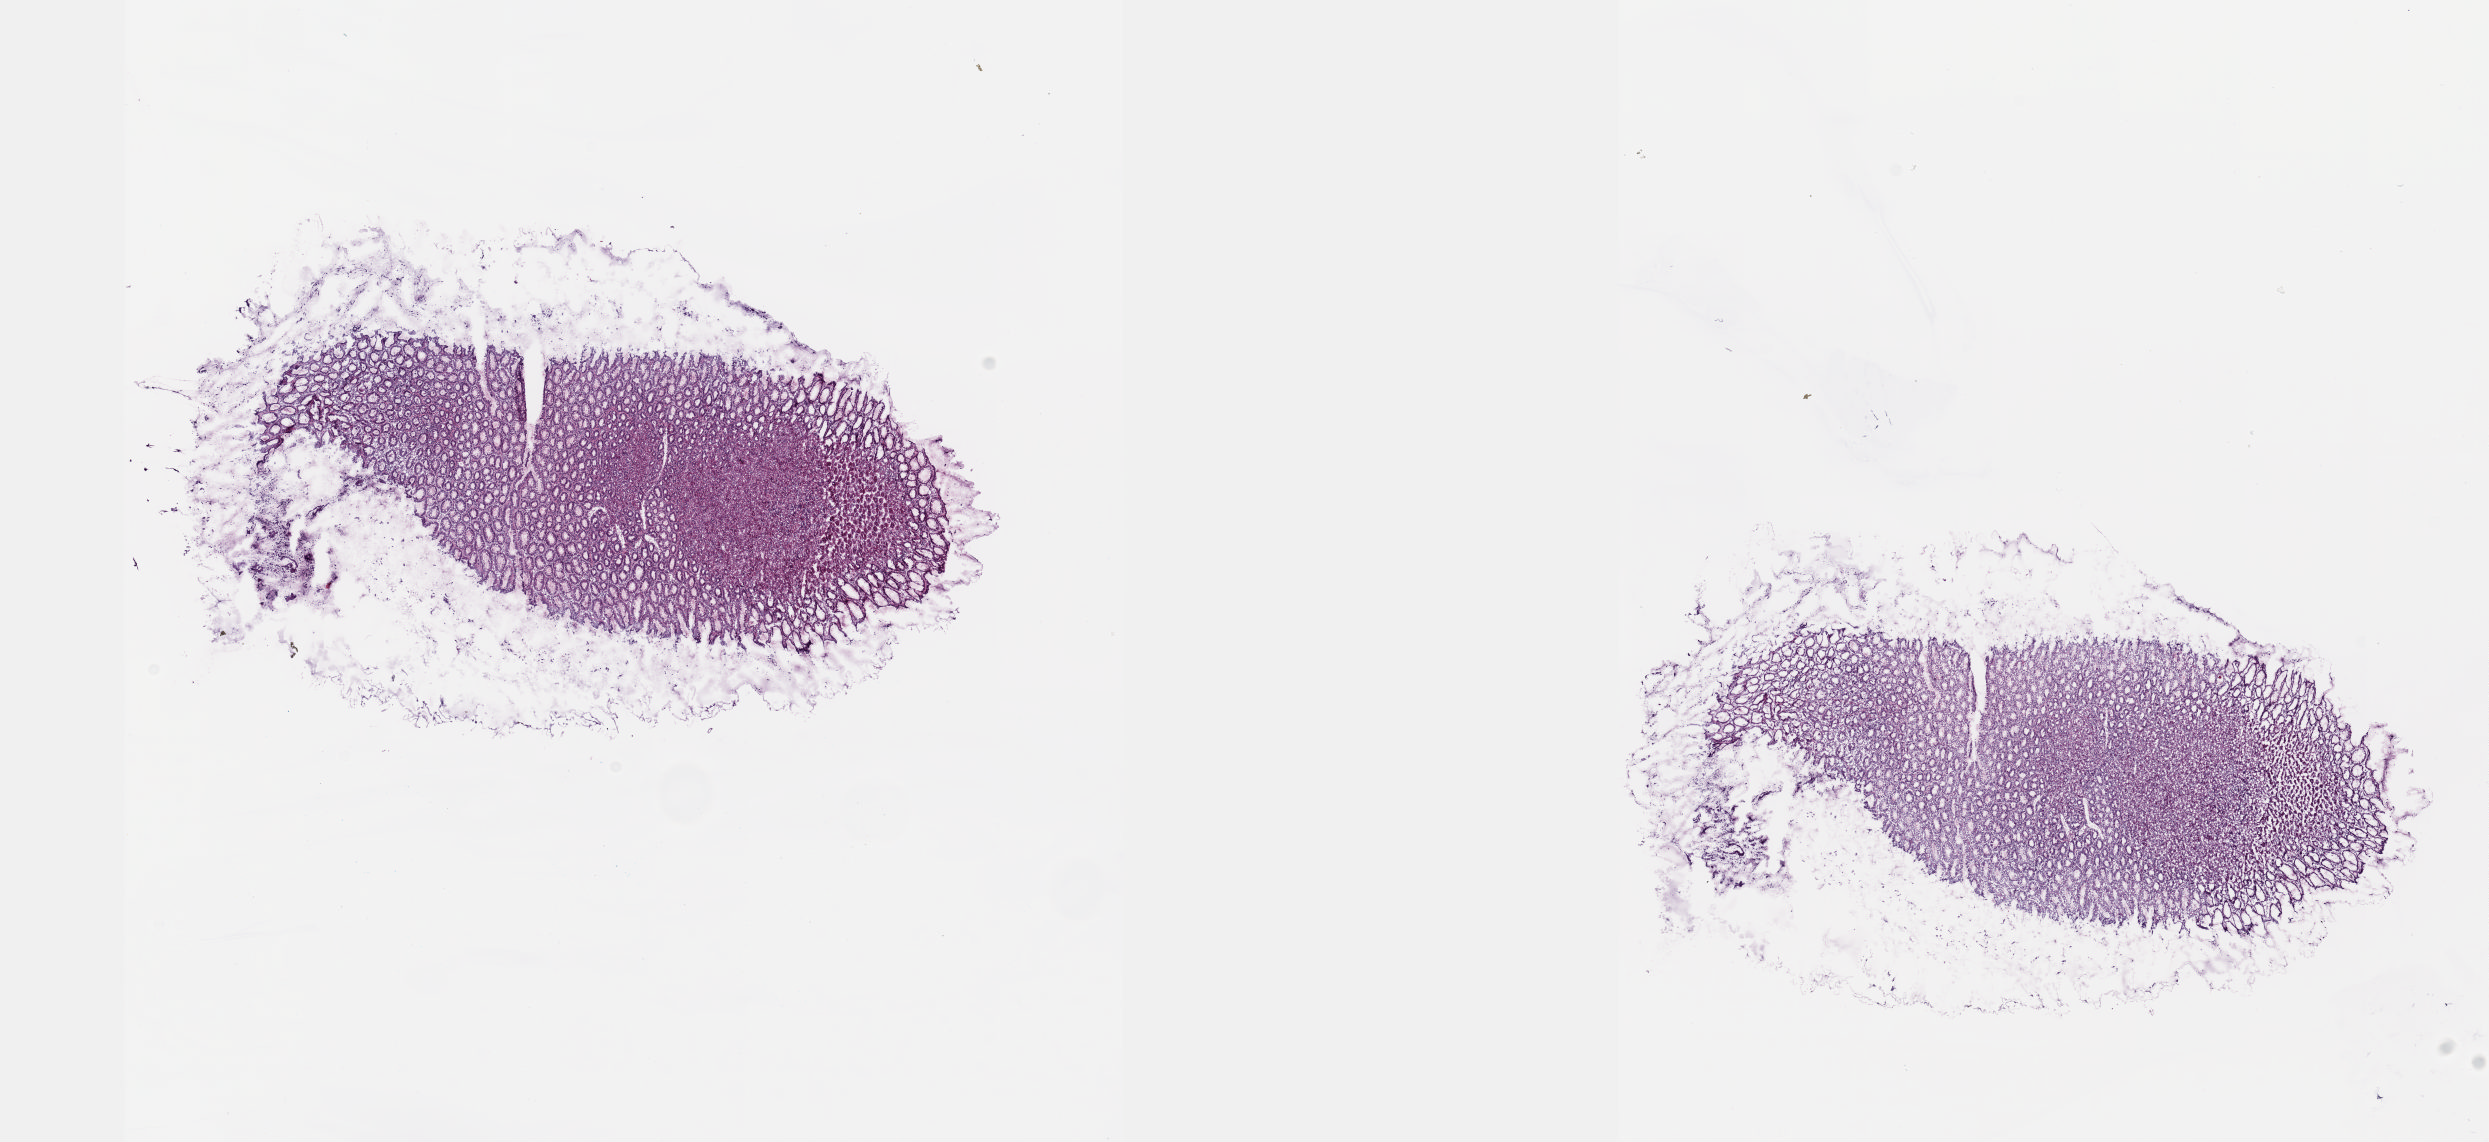
Whole-slide histology image, H&E, a low-resolution overview of the entire scanned area, about 20.1 x 9.2 mm, frozen section from the top of the tissue portion, solid tissue normal (non-tumour tissue) sample from the esophagus. Female patient; age at initial diagnosis 70 years. Slide review estimates, as recorded: tumour cells 0%, tumour nuclei 0%, normal cells 100%, stromal cells 0%, necrosis 0%. Infiltration values recorded for this section: lymphocyte infiltration 3%, monocyte infiltration 0%, neutrophil infiltration 0%.
• this section: solid tissue normal (non-tumour) sample from the same patient
• patient diagnosis: Squamous cell carcinoma, NOS